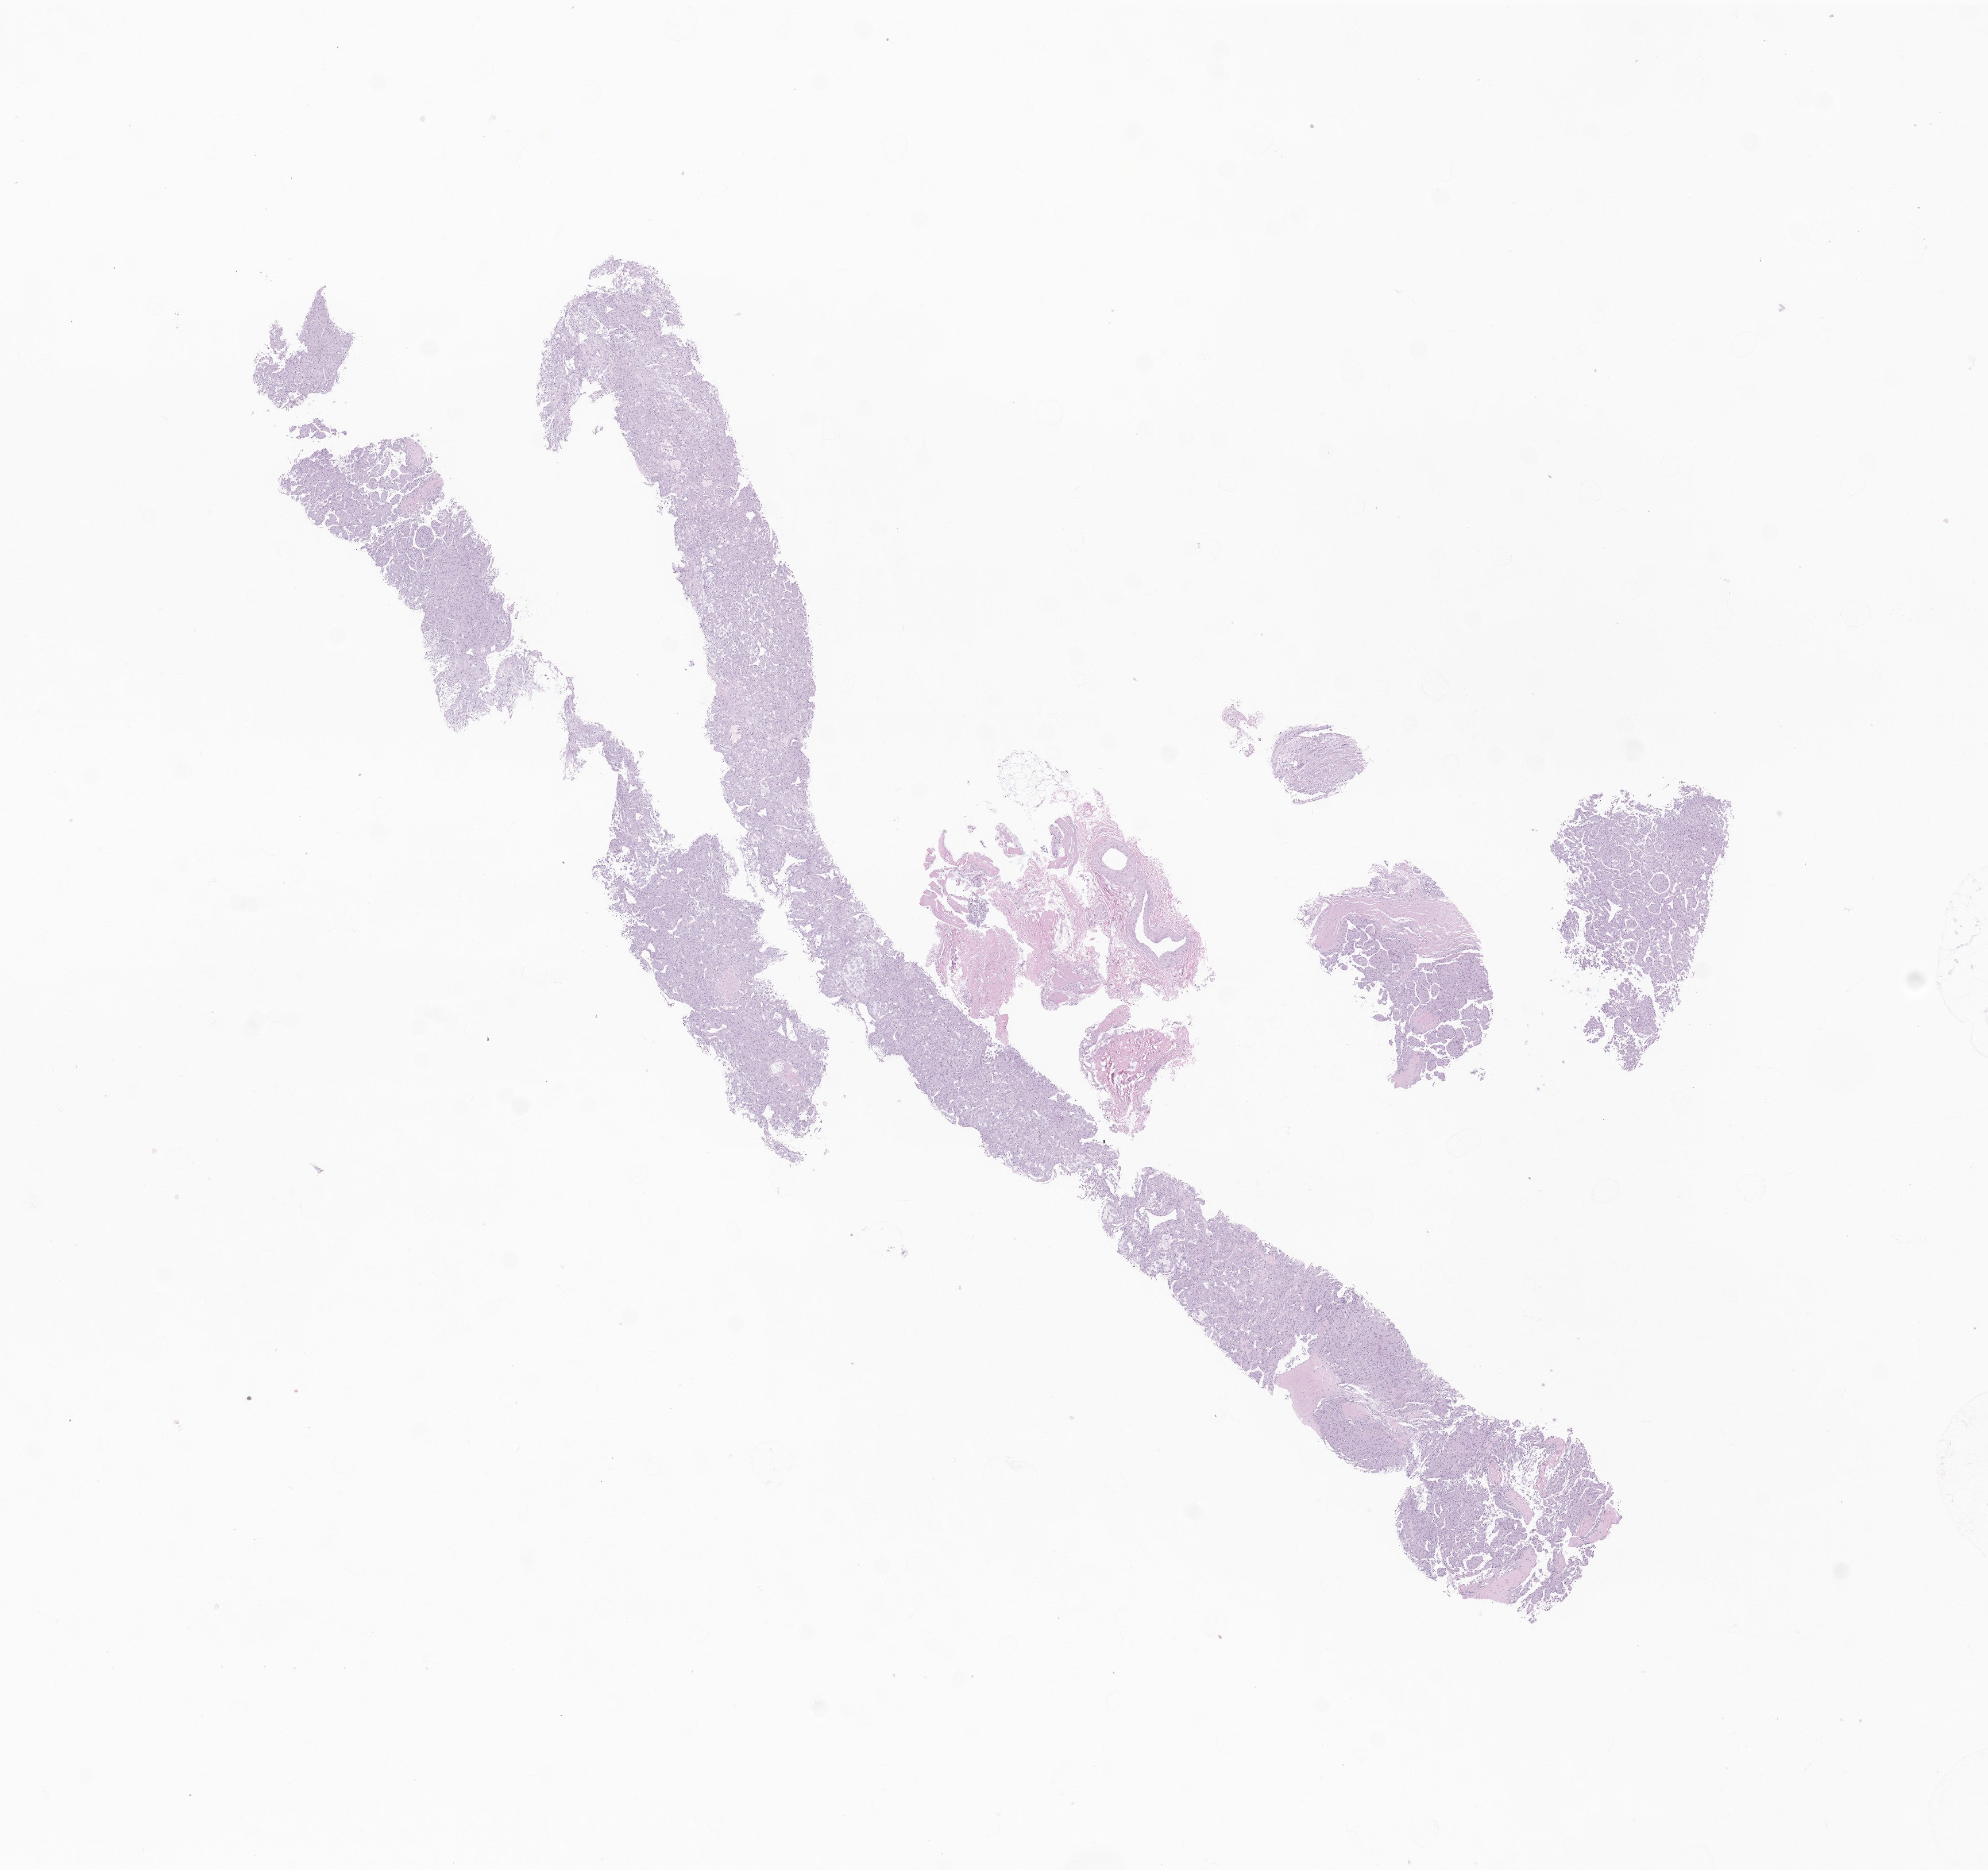
Digitized H&E-stained section of tumor tissue from the soft tissue of lower extremity, shown as a low-resolution overview of the whole scanned area (about 14.6 x 13.7 mm), formalin-fixed, paraffin-embedded (FFPE) tissue. Female patient, age 198 months (16 years 6 months).
Recorded diagnosis: Alveolar soft part sarcoma.